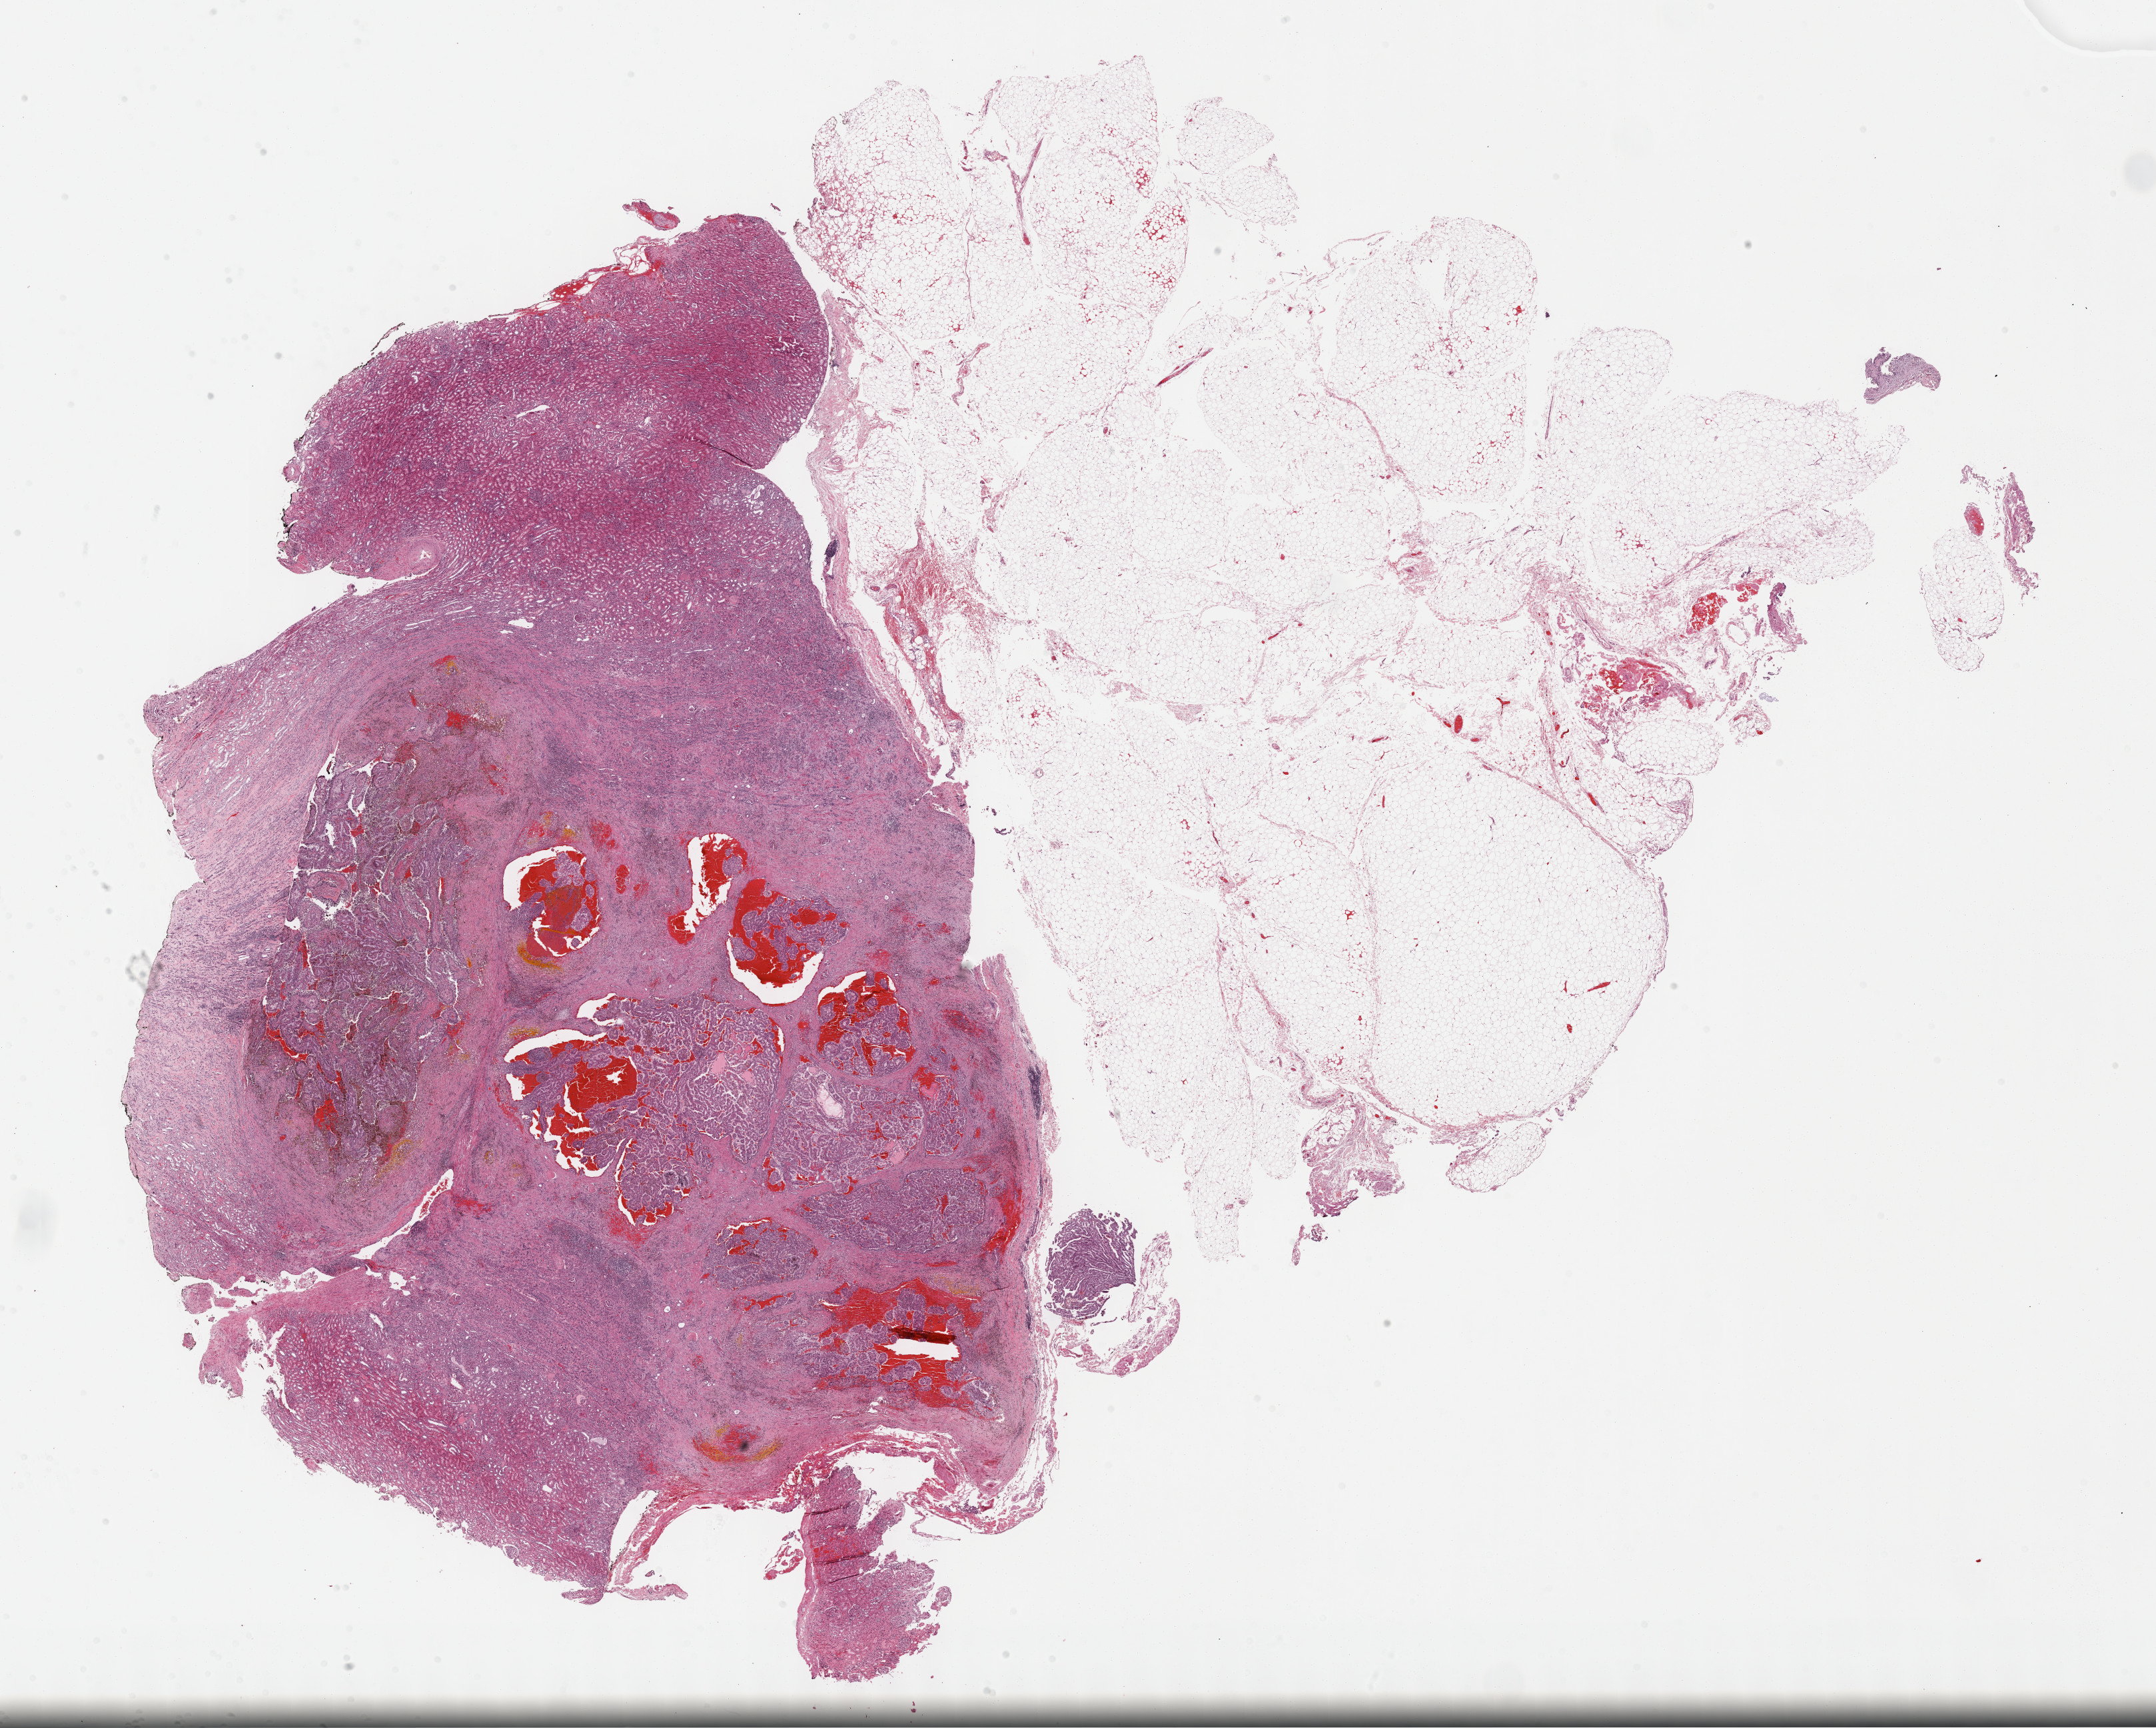
Digitized H&E tissue section (whole slide) — low-resolution overview of the scanned area, about 26.2 x 21.0 mm. Formalin-fixed paraffin-embedded (FFPE) diagnostic section. Sample: primary tumour, kidney. Female, age 68 years at initial diagnosis.
Laterality: left. Histologic diagnosis: Papillary adenocarcinoma, NOS. AJCC pathologic stage: I (7th edition).